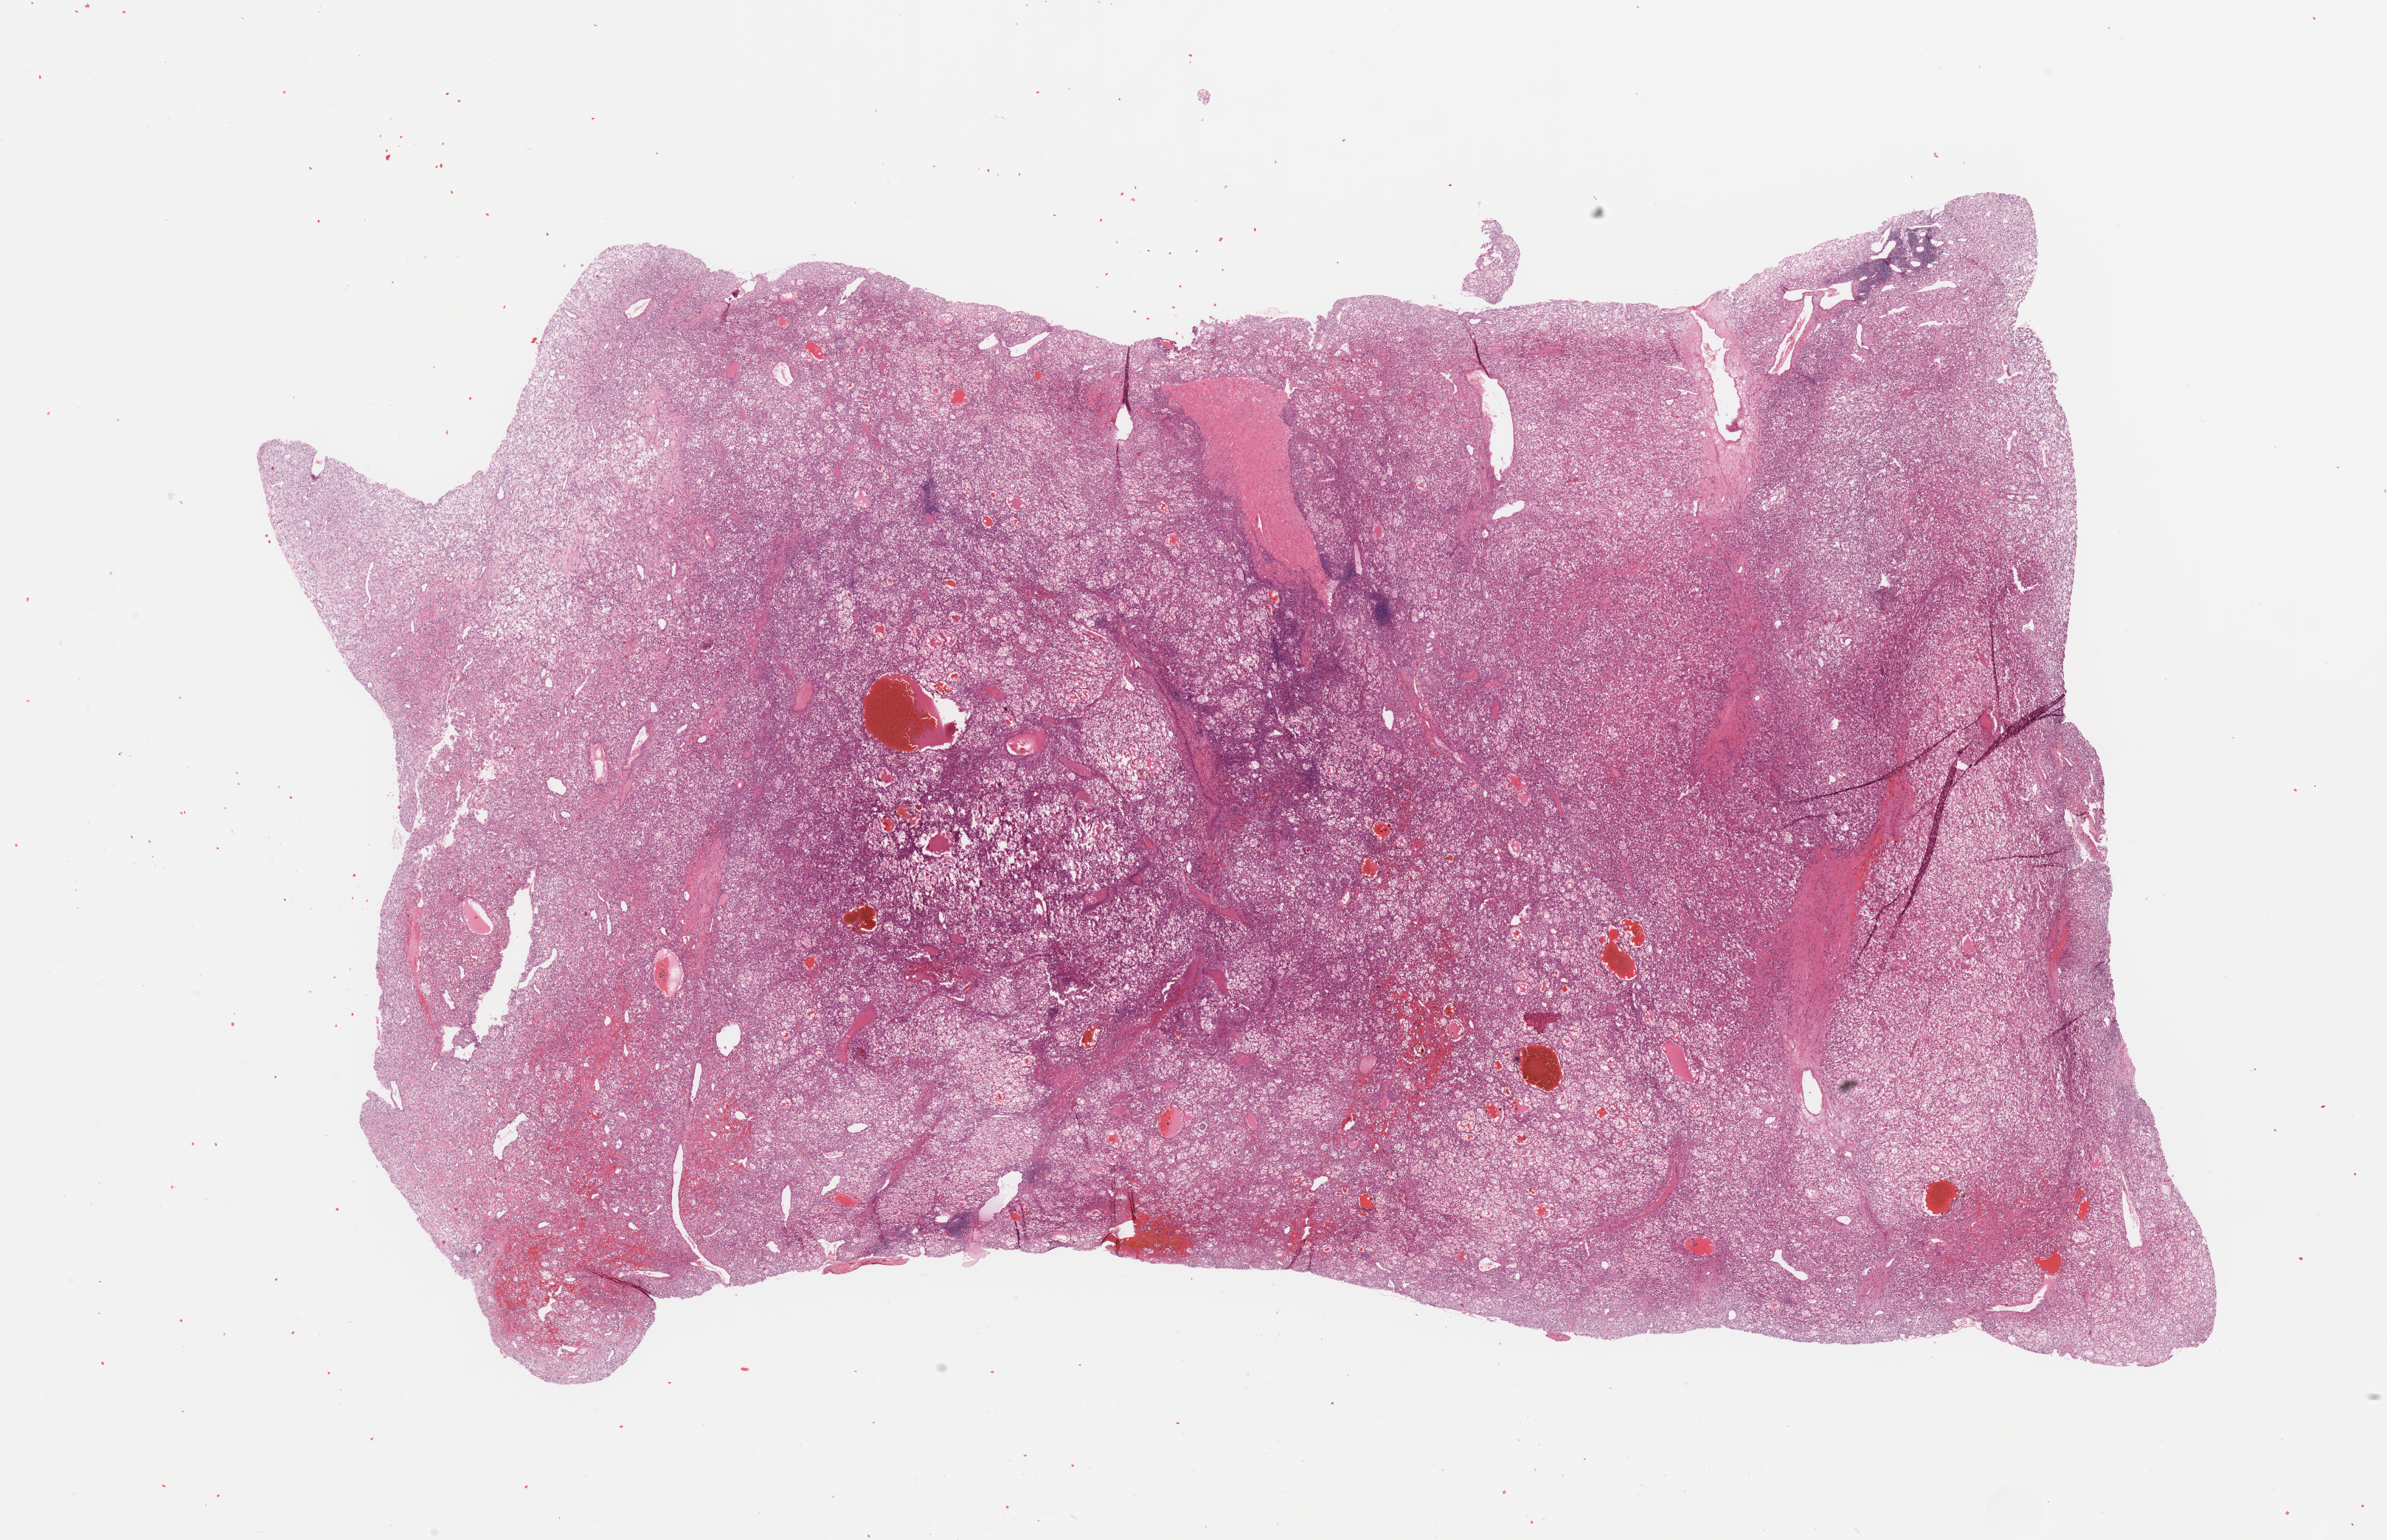
Hematoxylin and eosin (H&E) stained whole-slide image, a low-resolution overview of the entire scanned area, about 25.6 x 16.5 mm, tumour tissue sample, kidney. 42-year-old female patient. Histologic grade: G2 (moderately differentiated).
* histologic diagnosis: Renal cell carcinoma, NOS